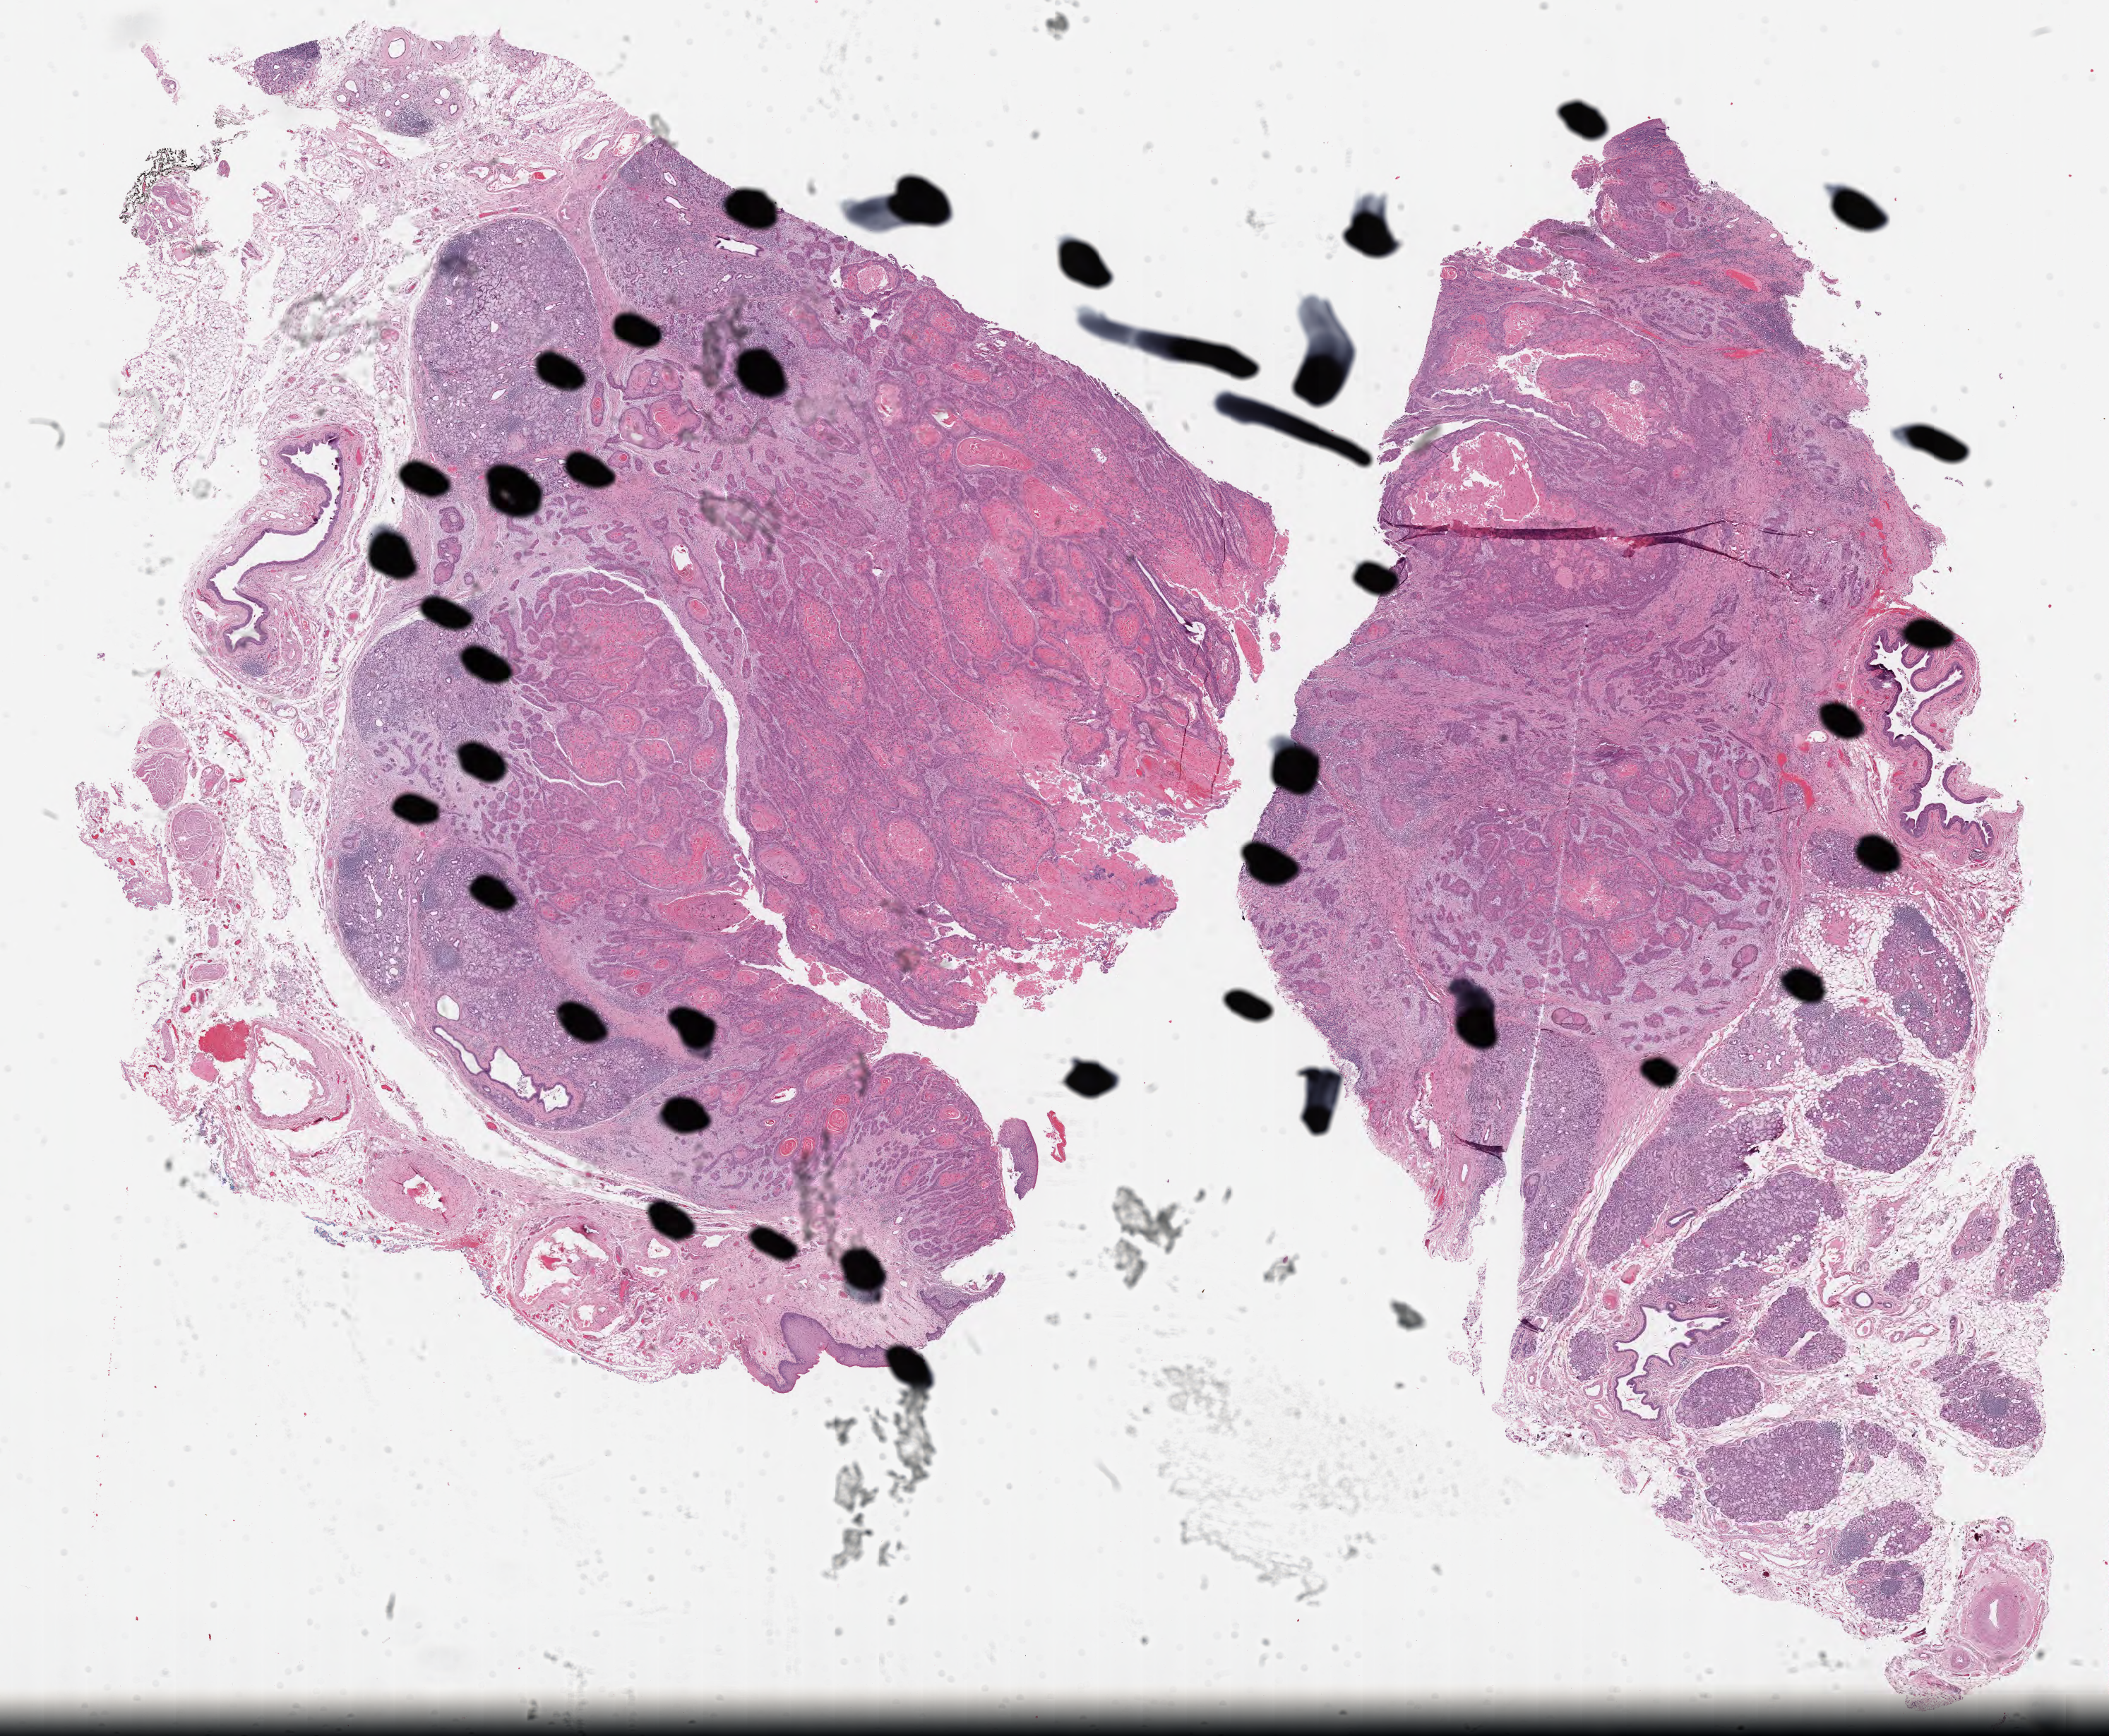
Hematoxylin and eosin (H&E) stained whole-slide image — a low-resolution overview of the entire scanned area, about 23.5 x 19.4 mm, formalin-fixed paraffin-embedded (FFPE) diagnostic section, sample: primary tumour, head and neck. Female patient; age at initial diagnosis 79 years. Histologic grade: G2 (moderately differentiated).
AJCC pathologic stage: IVA (6th edition). Histologic diagnosis: Squamous cell carcinoma, NOS (lower gum).